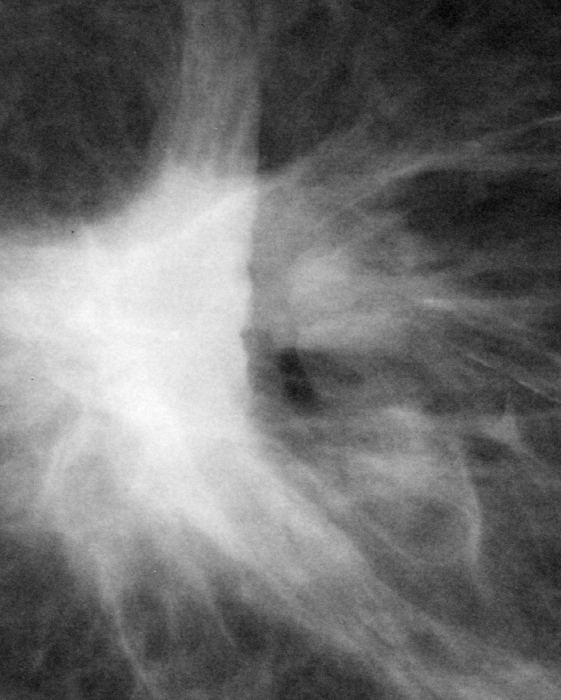
Cropped region of a digitized screen-film mammogram centred on a radiologist-marked abnormality; left breast; MLO view.
Mass, shape irregular, margins spiculated; BI-RADS assessment category 5; pathology result (as recorded, not read from the image): malignant.